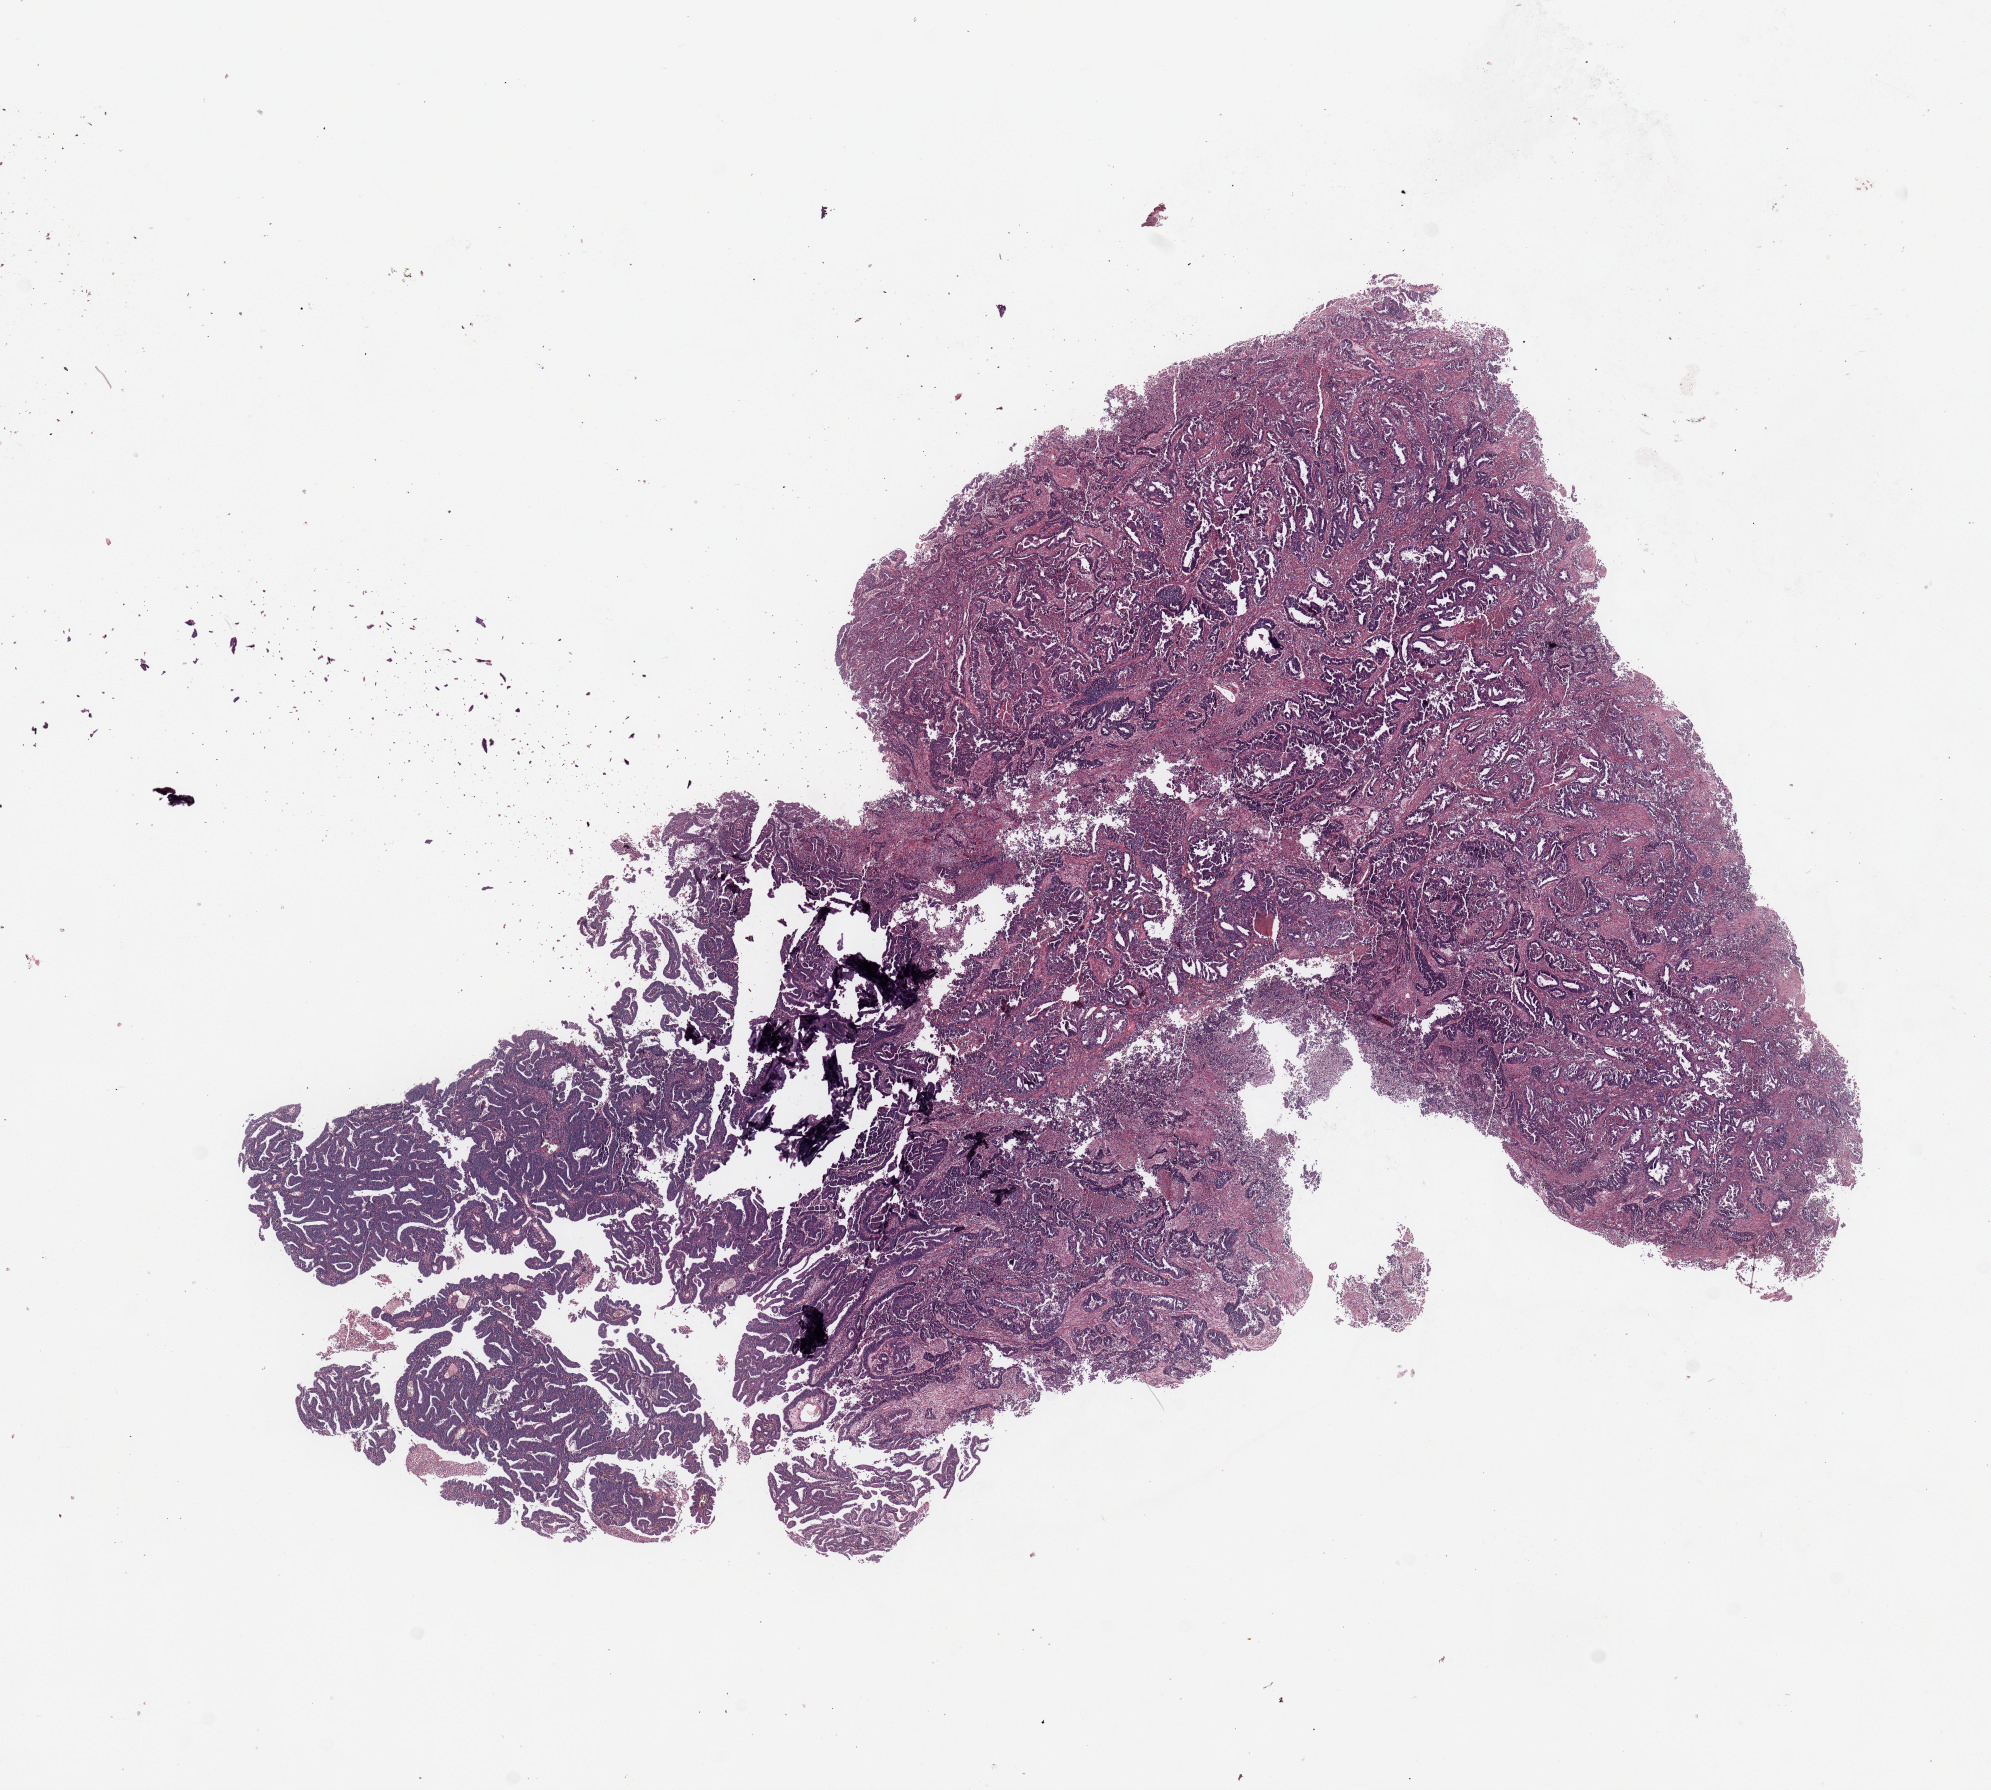
Hematoxylin and eosin (H&E) stained whole-slide image — a low-resolution overview of the entire scanned area, about 15.8 x 14.2 mm. Uterus, tumour tissue. 55-year-old female patient. Histologic grade: G3 (poorly differentiated).
* histologic diagnosis: Endometrioid adenocarcinoma, NOS
* AJCC pathologic stage: I